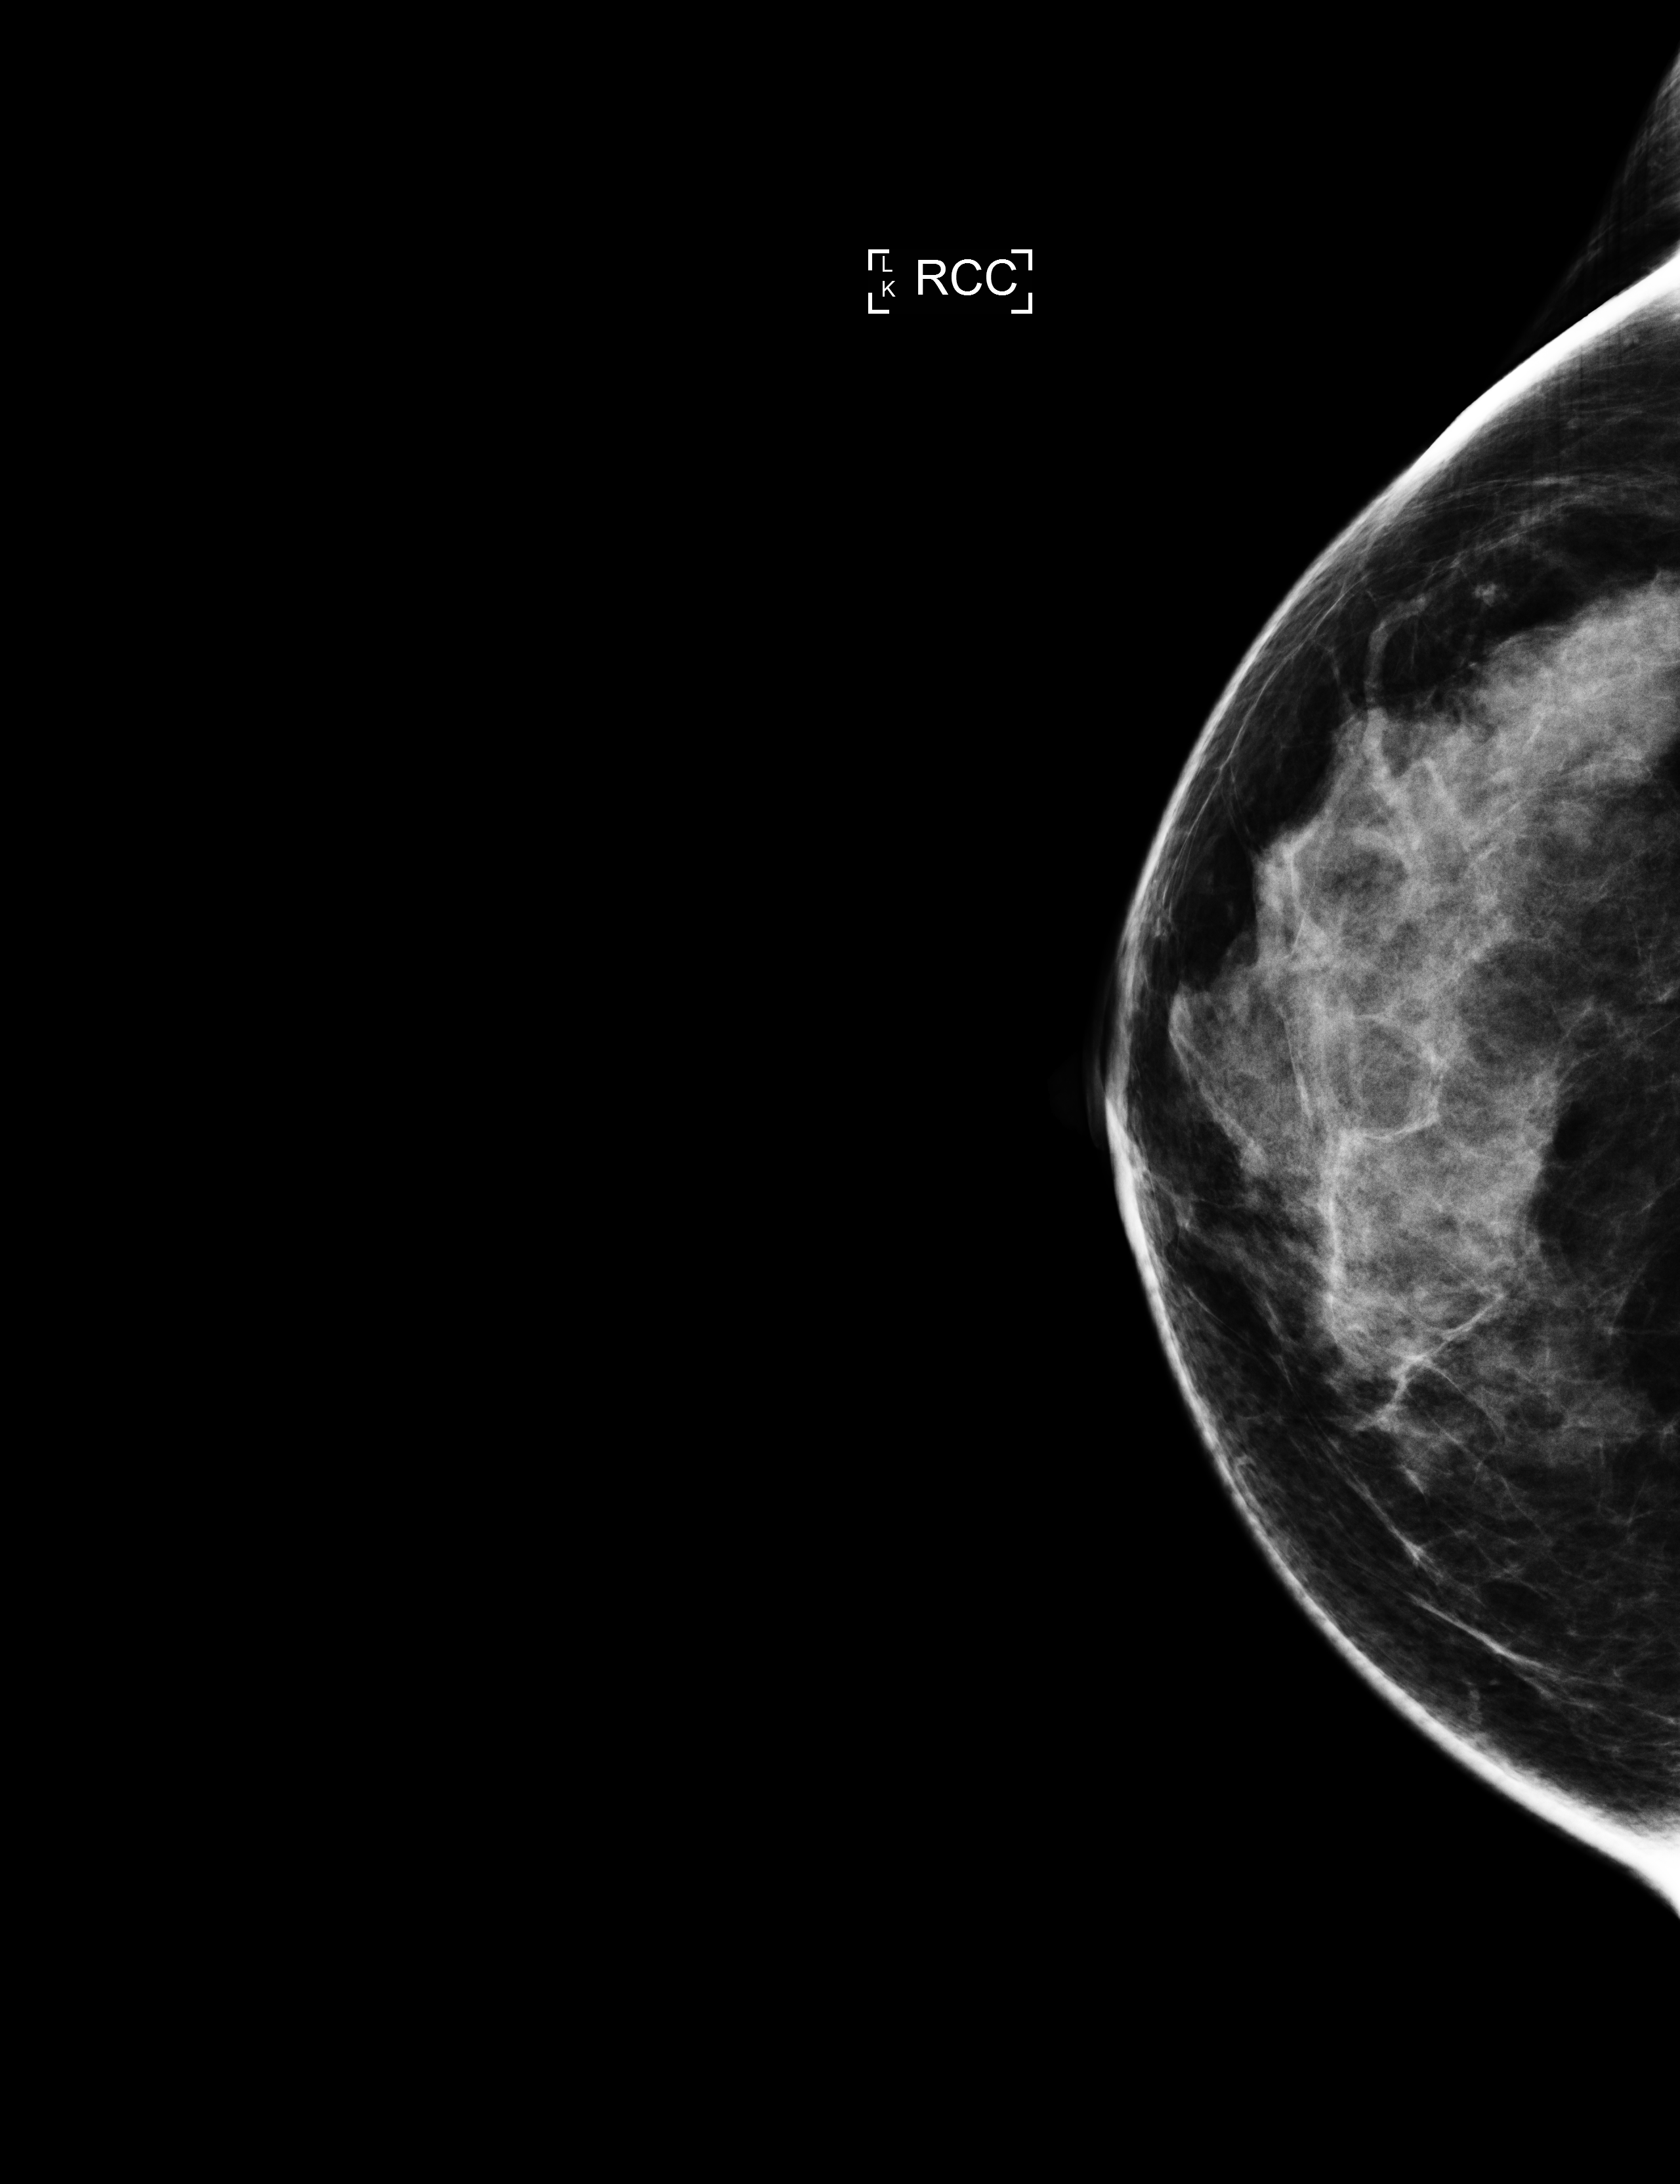
Annual screening mammography examination, compressed breast thickness 71 mm. Patient: female, 44 years.
Image type: full-field digital mammogram. Breast: right. Projection: cranio-caudal projection.